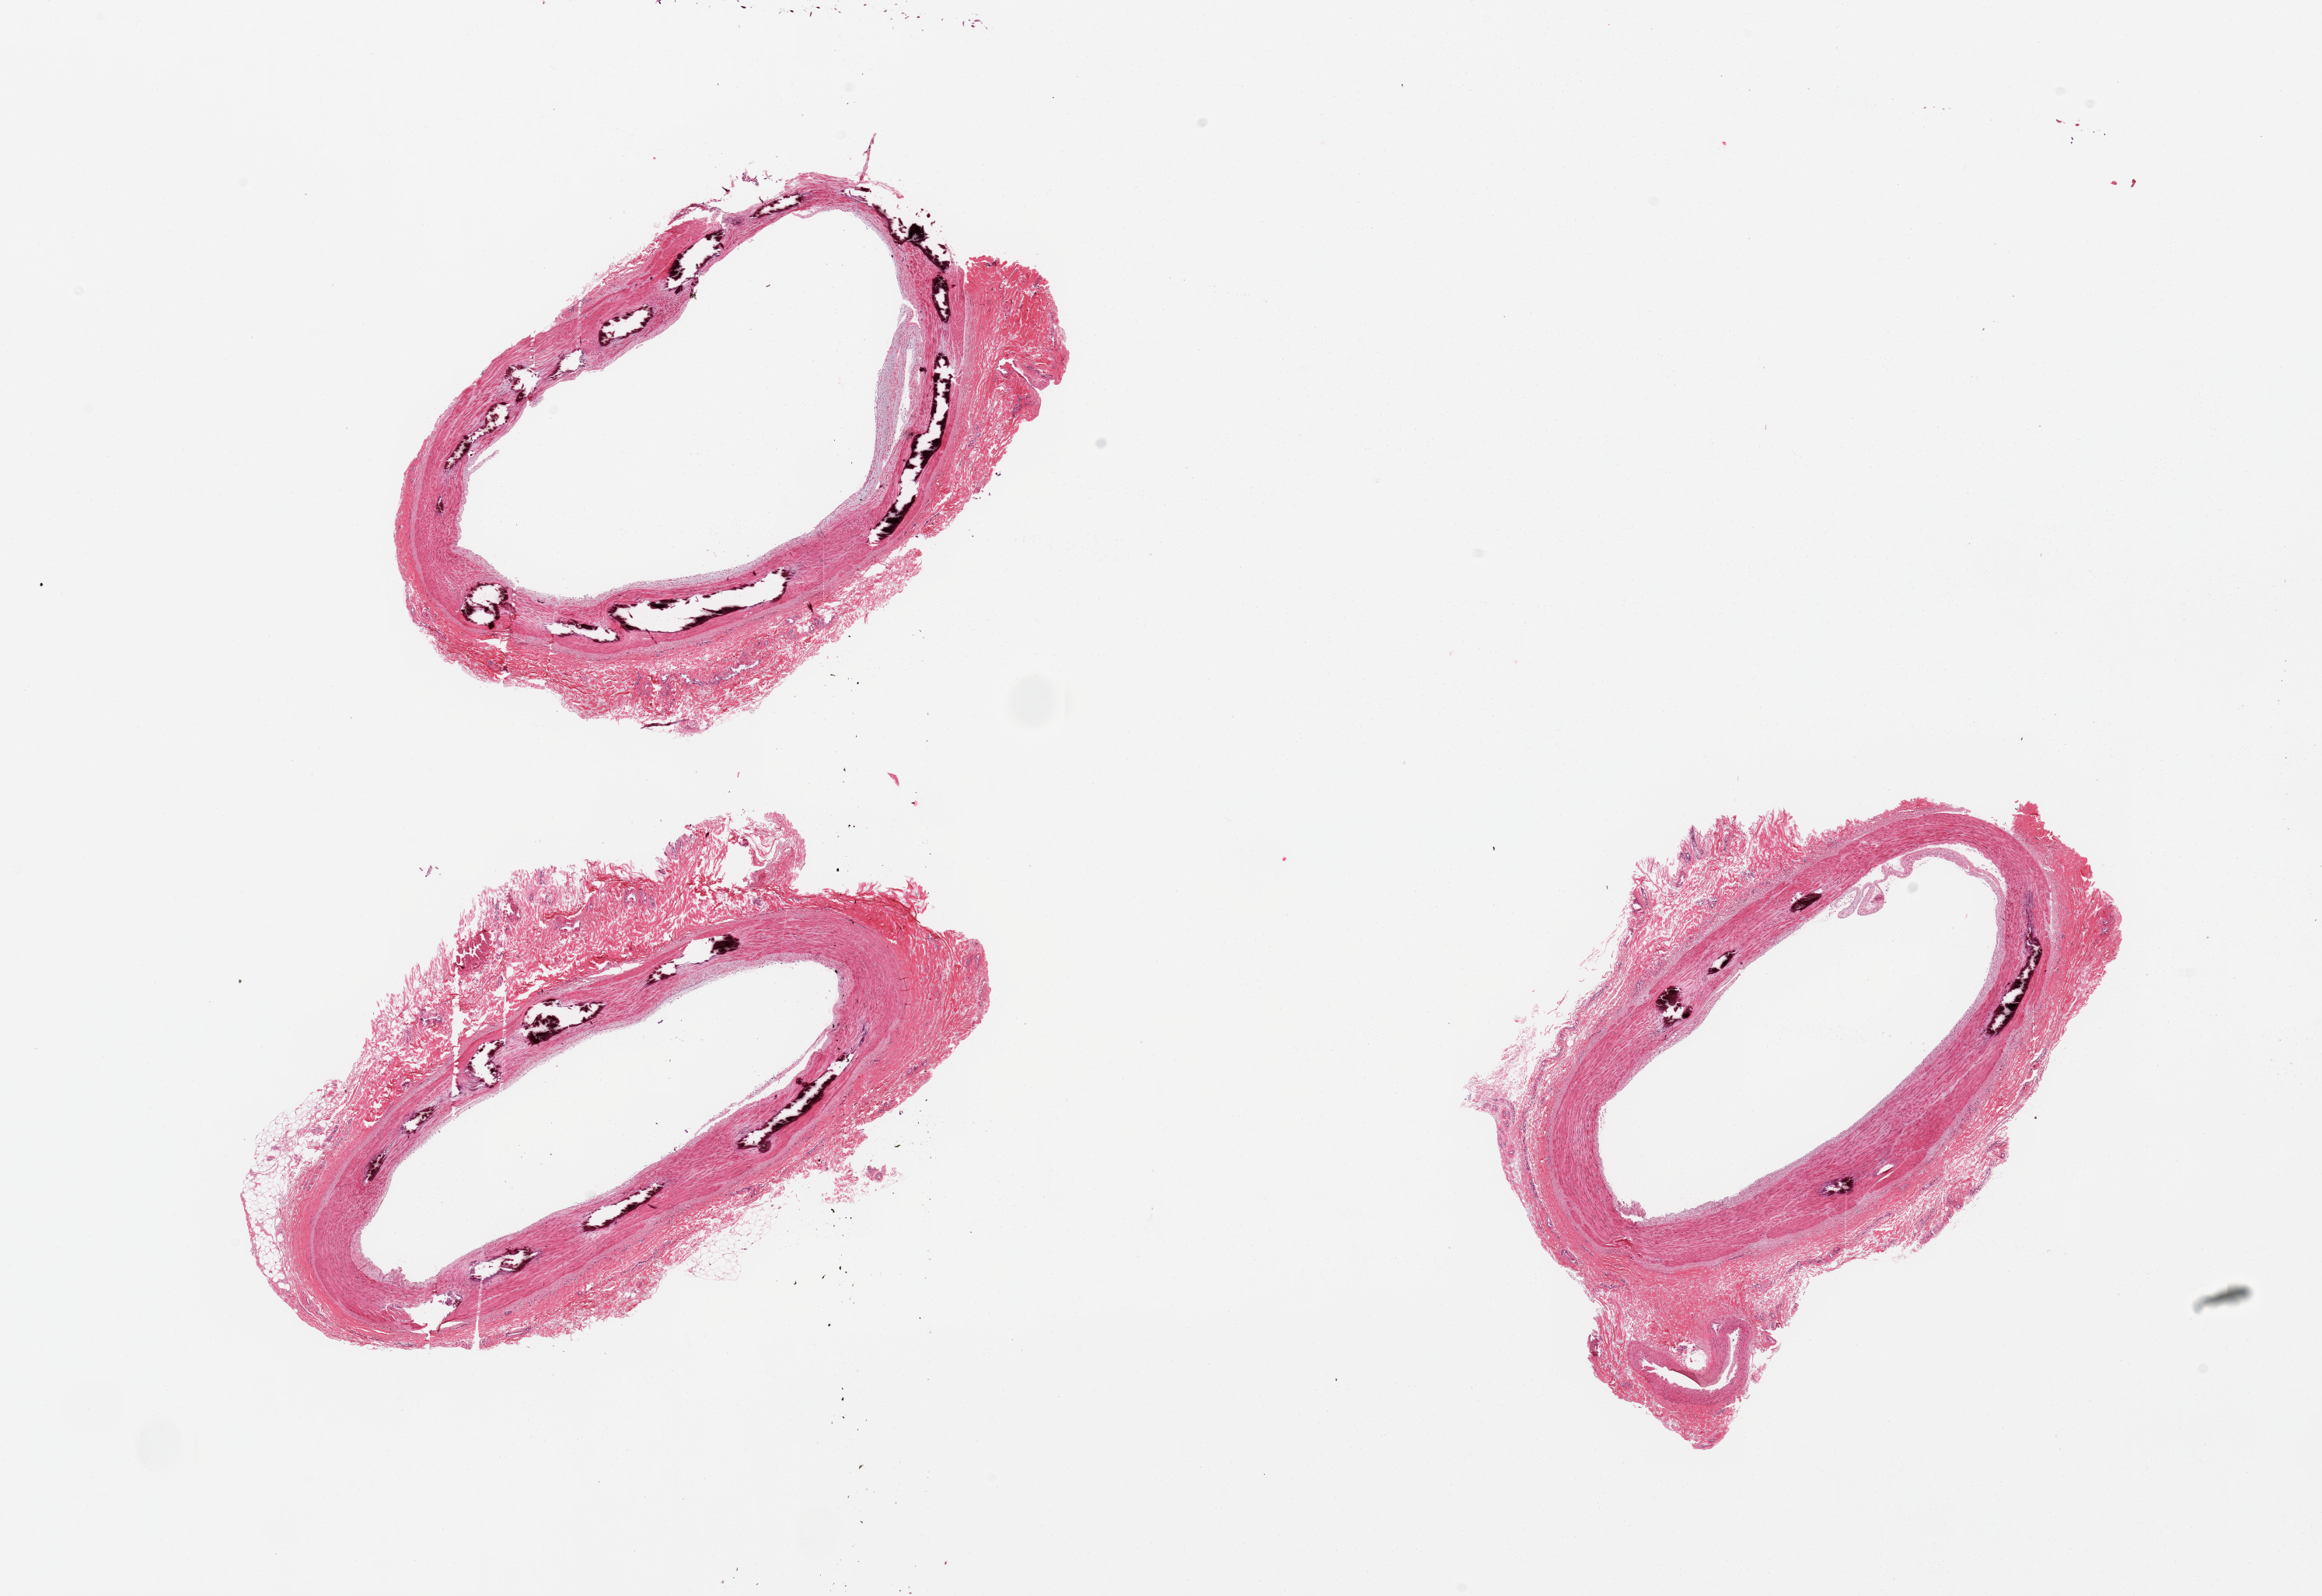
Whole-slide image, haematoxylin and eosin stain, shown as a low-resolution overview of the whole scanned area (about 23.6 x 16.2 mm); PAXgene-fixed paraffin-embedded (PFPE) section; sampled site (target tissue): tibial artery; donor tissue sample.
Reviewer comment on this tissue sample: 3 pieces; no plaque, but extensive medial calcification.